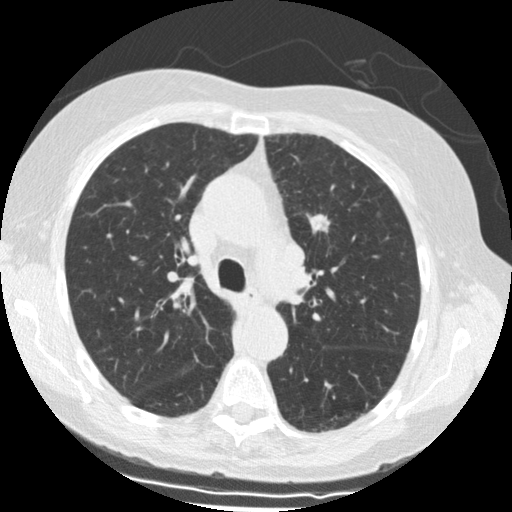
Axial slice from a low-dose chest CT screening exam. First (baseline) screen. Lung window (W 1500 / L -600 HU). 2.5 mm slice thickness. Slice 44 of 139 in the series. 512 × 512 image matrix, field of view 318 × 318 mm. Female, age 69 years at enrolment.
Lesion marked by an expert reader, bounding box [x1, y1, x2, y2] px = [299, 205, 344, 244]. The screening reader recorded 2 non-calcified nodules or masses ≥4 mm on this exam; which of them this box marks is not recorded. Lung cancer was diagnosed 18 days after this screen: squamous cell carcinoma, NOS, left upper lobe, stage IIIA (AJCC 6th edition), 15 mm at pathology.